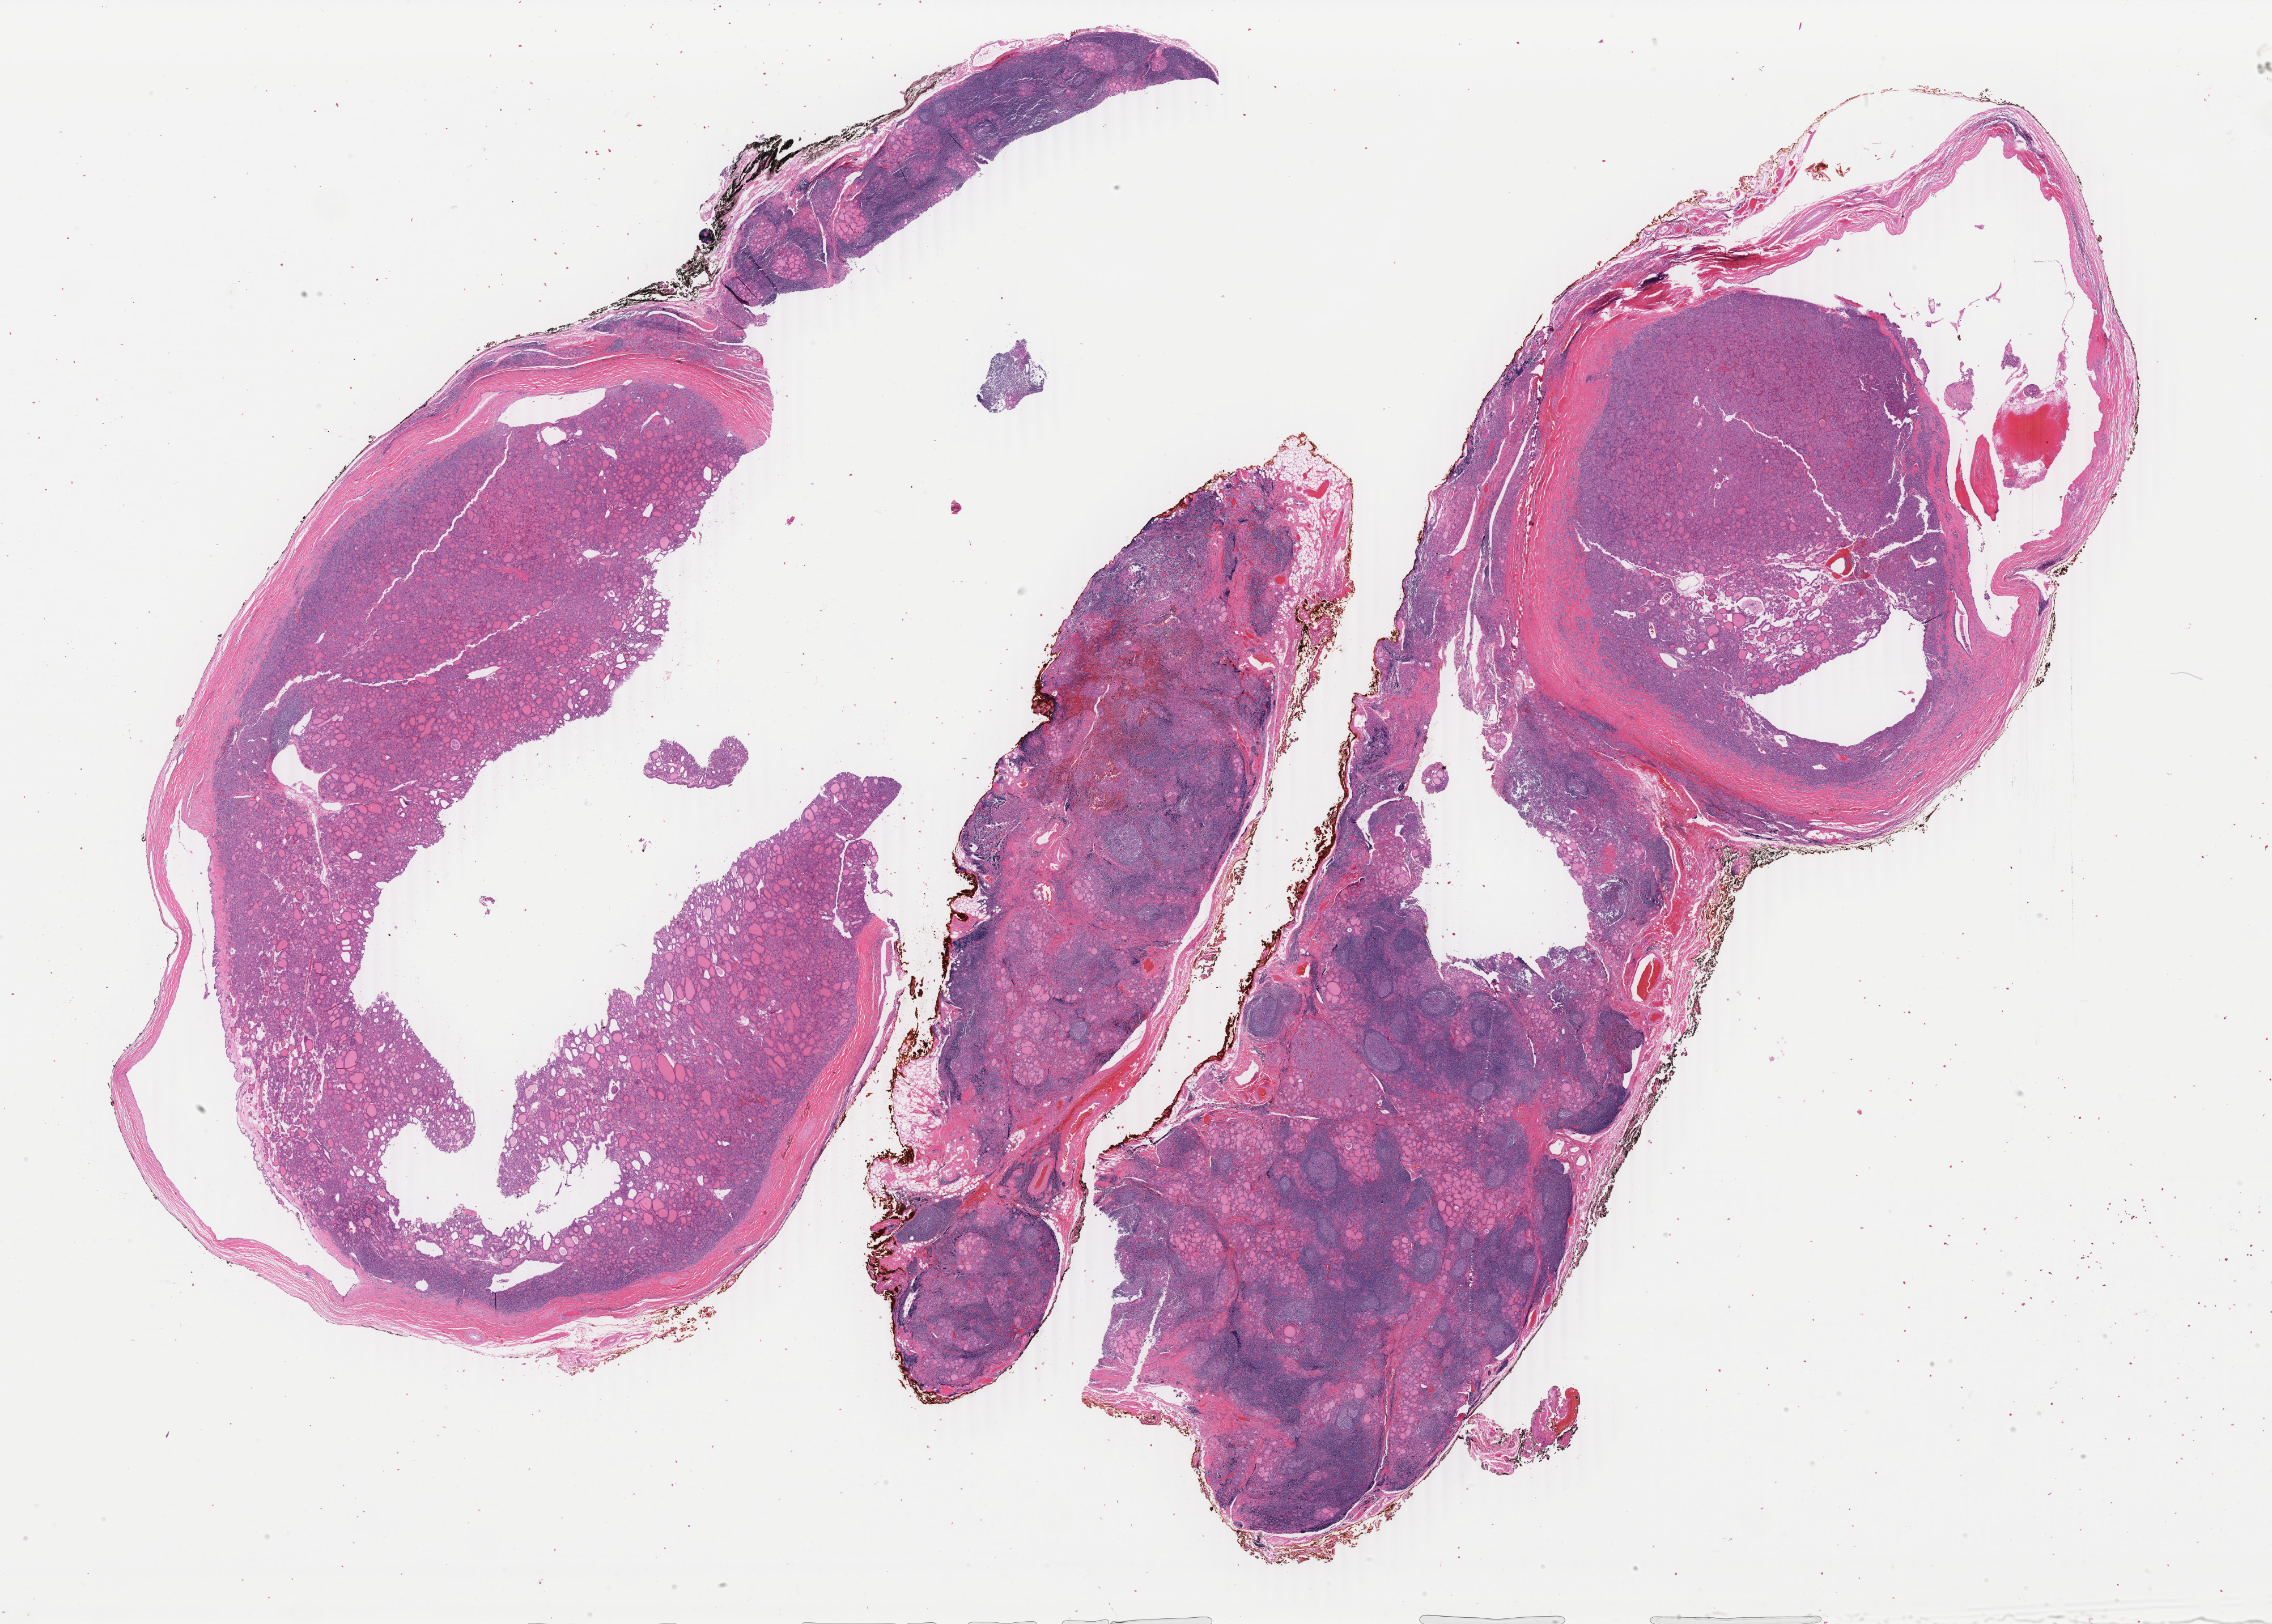
Whole-slide histology image, Hematoxylin and eosin (H&E) stained — a low-resolution overview of the entire scanned area, about 31.9 x 22.8 mm (from a 40x scan), FFPE section, primary tumour sample from the thyroid. Patient: female, age at initial diagnosis 37 years.
Laterality: left. Lymph nodes positive (case pathology): 0 of 1 examined. AJCC pathologic stage: I (6th edition). Pathologic diagnosis: Papillary carcinoma, follicular variant (thyroid gland).